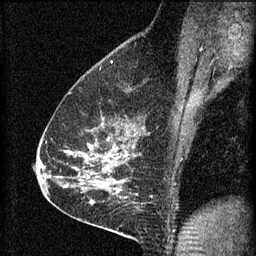
Breast MRI (dynamic contrast-enhanced), one sagittal slice; 3 images stored at this slice position (order not interpretable as contrast timing); 1.5 T; TE 4.2 ms, TR 8.2 ms; 2 mm slice thickness; 256 × 256 image matrix, field of view 180 × 180 mm. Patient: female, 59 years.
Structures marked on this image (semi-automatically segmented with operator editing):
- analysis volume of interest (the breast-tissue region the enhancement analysis was run in; not a lesion): bounding box (x1, y1, x2, y2) in pixels: (61, 106, 134, 161)
- tumour enhancement mask (voxels above the 70 % enhancement threshold inside the analysis volume of interest): (91, 148, 119, 159)